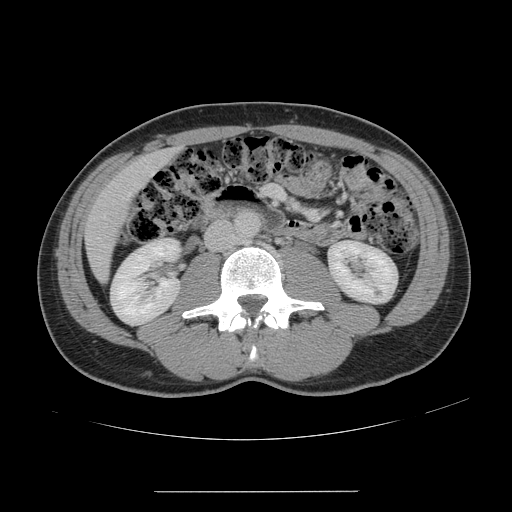
Contrast-enhanced abdominal CT, one axial slice; position 42 of 178 along the scan axis; intravenous contrast given; soft-tissue window (W 400 / L 40 HU); 512 × 512 image matrix, field of view 401 × 401 mm. Male patient, age 53 years. Case-level facts recorded for this patient, not image findings: diagnosis: colorectal cancer liver metastases, imaged before liver resection; multiple liver metastases: yes; largest metastasis: 2.4 cm; chemotherapy before resection: yes.
Annotated regions visible in this slice (manually delineated by an expert):
- hepatic veins: bounding box (x1, y1, x2, y2) in pixels: (103, 172, 154, 218)
- liver: (86, 150, 175, 280)